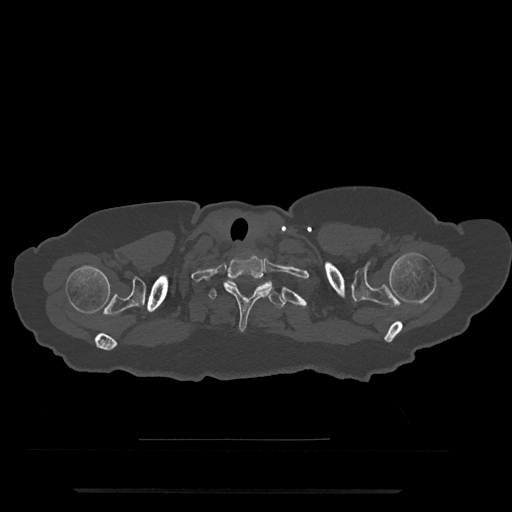
CT including the spine, one axial slice; slice 701 of 797 in the series (ordered by position); 120 kVp; bone window (W 1800 / L 400 HU); 512 × 512 image matrix. Patient: female, 51 years. Case-level facts recorded for this patient, not image findings: primary cancer: neuro; vertebrae with lytic lesions (as recorded): T8.
Structures marked on this image (semi-automatic segmentation, software-assisted and operator-edited):
- T1 vertebra: box from (x=223, y=255) to (x=274, y=332) px
- T2 vertebra: (x=209, y=279)–(x=286, y=309)